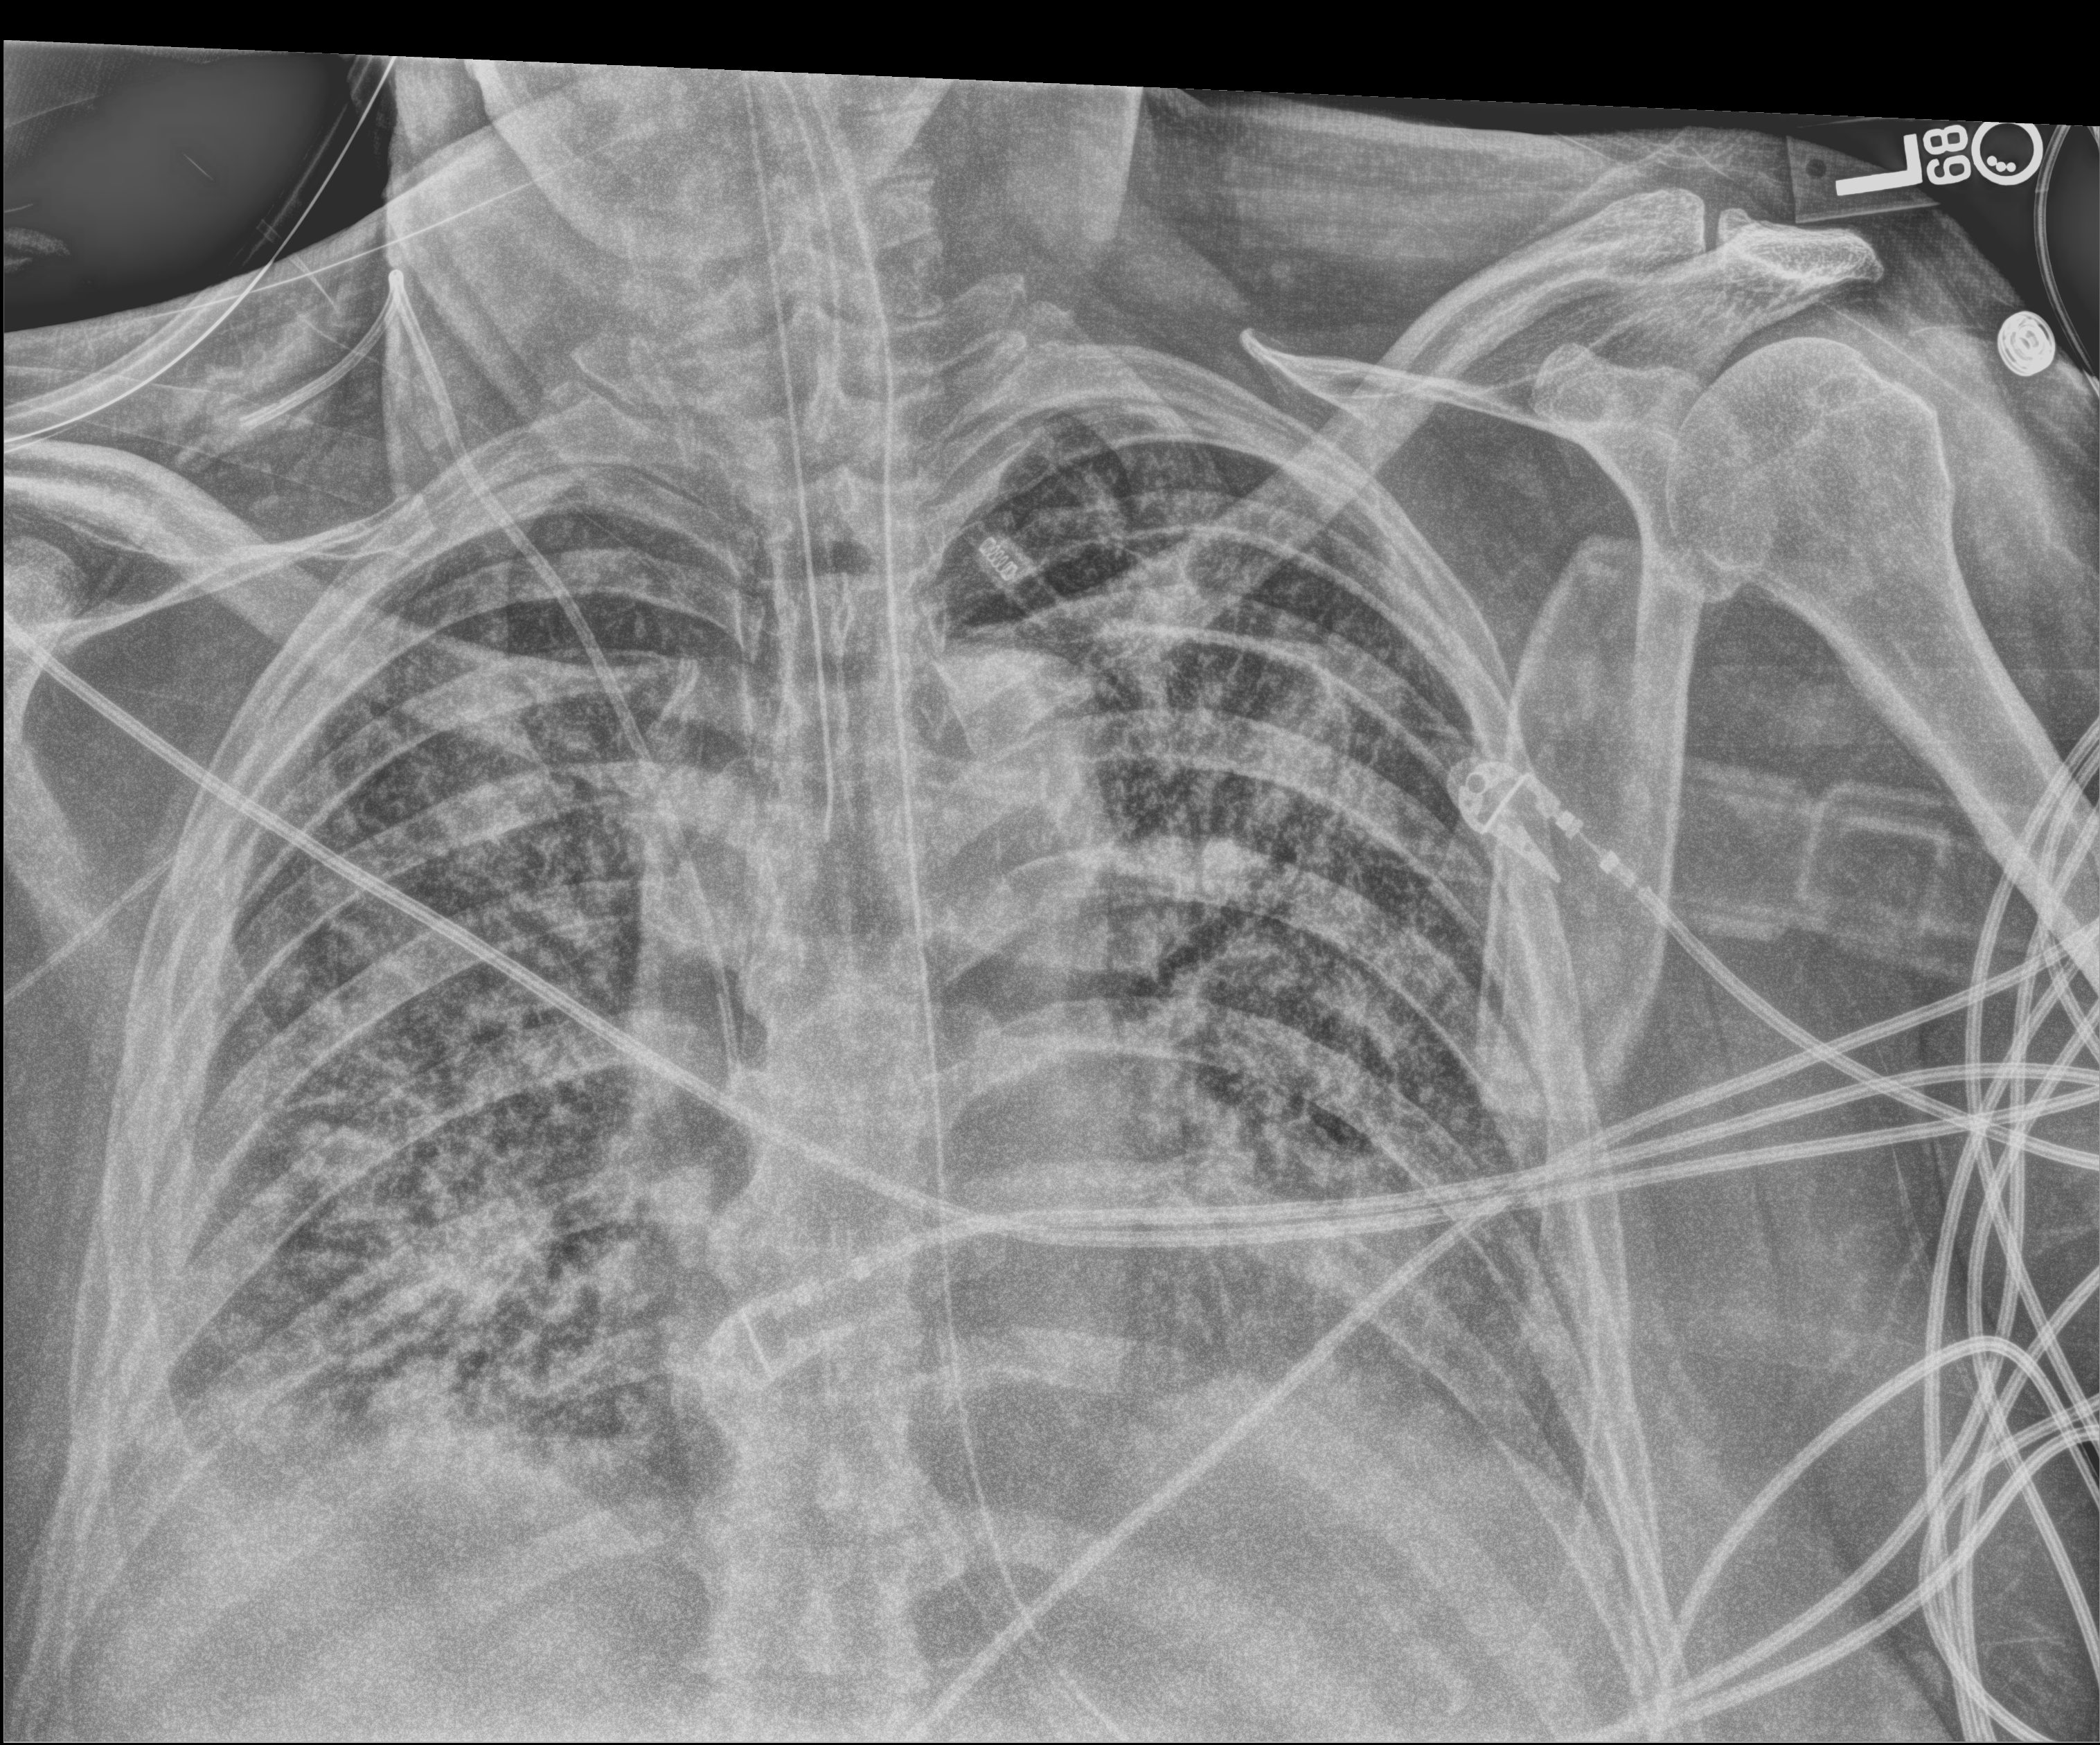
Bedside chest radiograph (digital radiography), anteroposterior (AP) projection. Male patient hospitalised with COVID-19, age 60–74 years.
From the hospital-stay record, not from the radiograph (when in the stay this image was taken is not recorded): length of hospital stay: 40 days; chronic kidney disease (admission record): no.